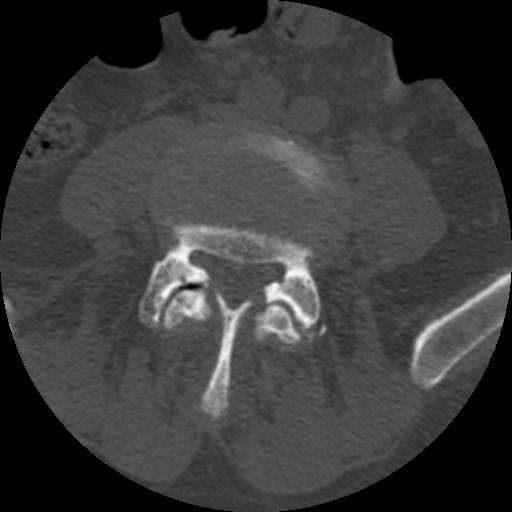
CT including the spine, one axial slice; slice 266 of 399 in the series (ordered by position); reconstruction kernel STANDARD; bone window (W 1800 / L 400 HU); 512 × 512 image matrix, field of view 160 × 160 mm. Patient age 71 years. From the clinical record (not read from this slice): primary cancer: prostate.
Structures marked on this image (semi-automatically segmented with operator editing):
- L4 vertebra: bounding box [x1, y1, x2, y2] px = [163, 129, 336, 349]
- L5 vertebra: [139, 218, 327, 419]